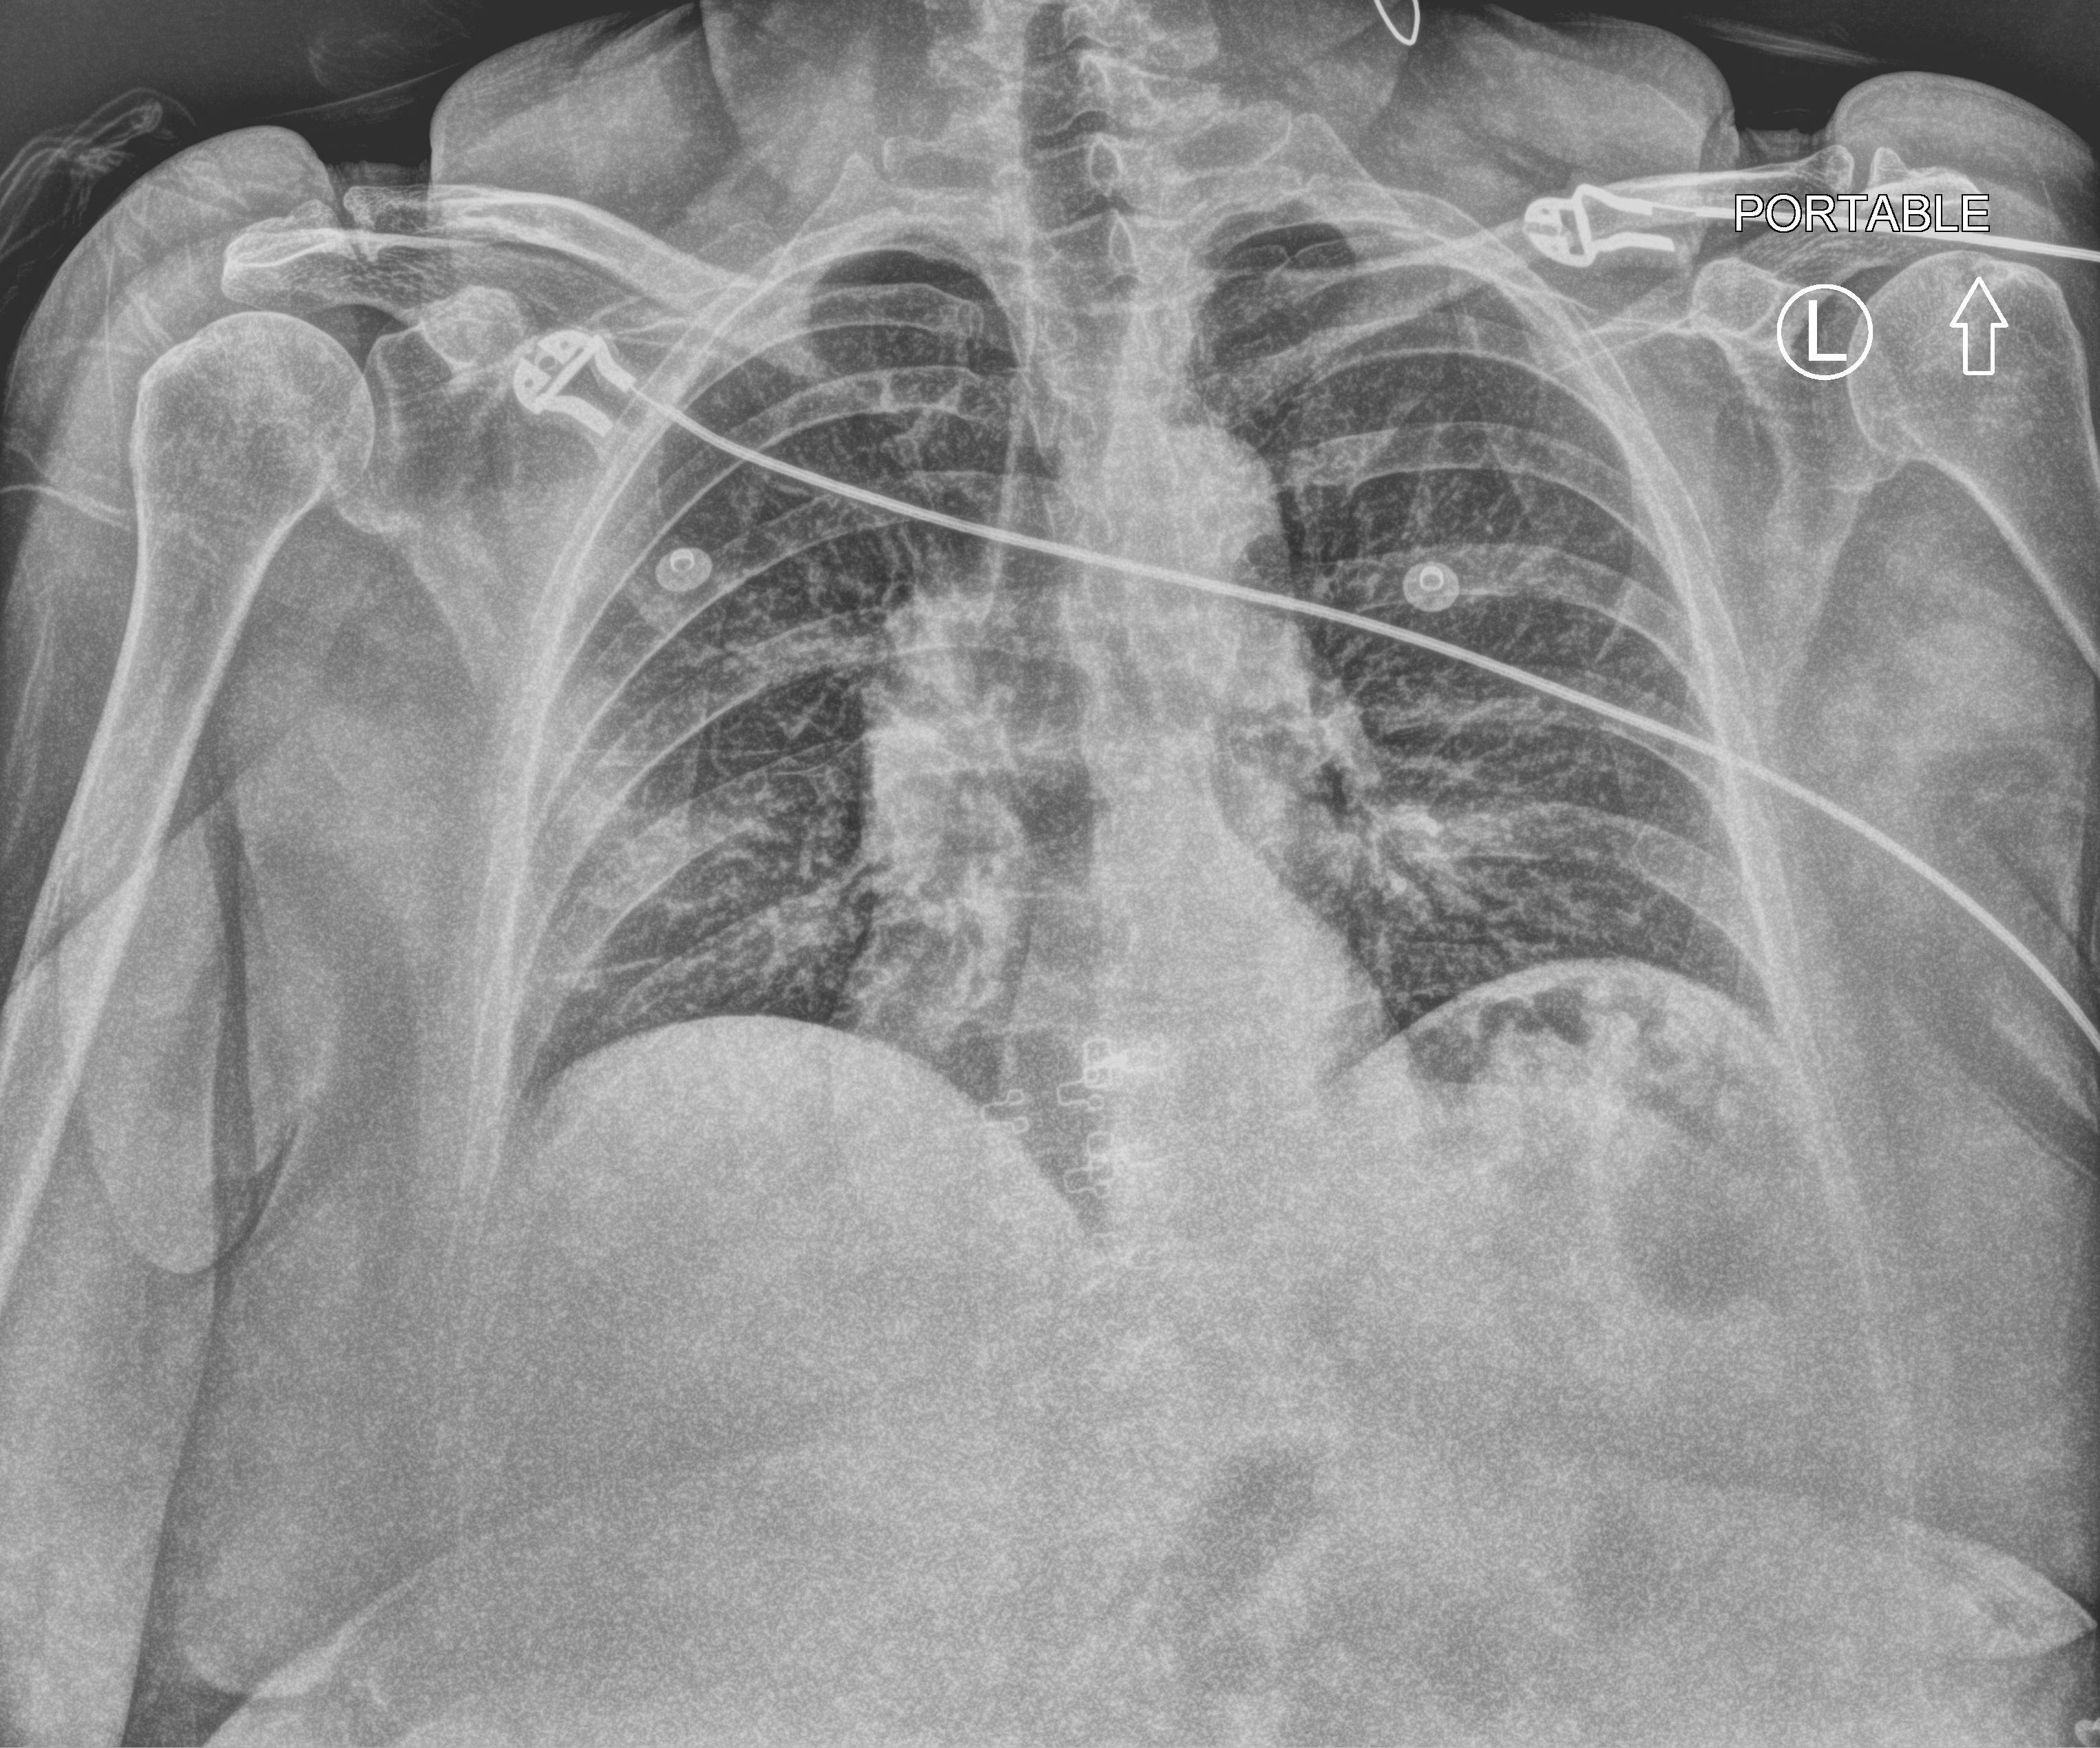
Bedside chest radiograph (computed radiography); anteroposterior (AP) projection. Patient hospitalised with COVID-19; female, aged 60–74 years.
Admission-level facts for this patient (not findings on this image; timing relative to this image not recorded): admitted to intensive care during this hospital stay: no.